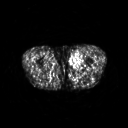
FDG PET of an extremity soft-tissue mass (from a PET/CT study), one axial slice; slice 244 of 311 in the series (ordered by position); 128 × 128 image matrix, field of view 500 × 500 mm. Male patient, age 29 years. Case-level facts recorded for this patient, not image findings: histological type: mixoid liposarcoma; grade: low; site of the primary tumour: left thigh.
Annotated regions visible in this slice (expert contour drawn on MRI and transferred to this co-registered scan by the dataset authors):
- gross tumour volume (mass): bounding box (x1, y1, x2, y2) in pixels: (69, 53, 82, 69)